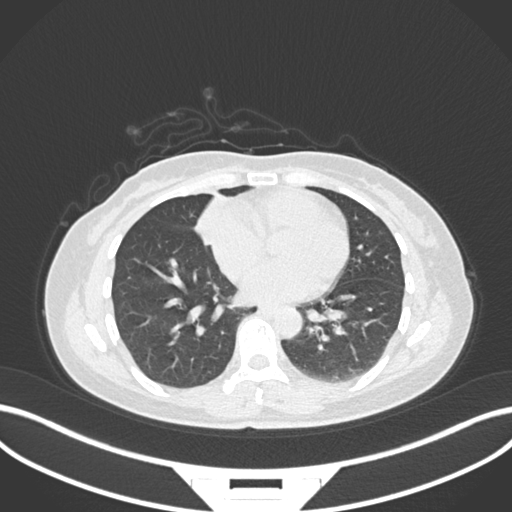
Chest CT, one axial slice. Position 61 of 171 along the scan axis. Reconstruction kernel B30f. Lung window (W 1500 / L -600 HU). 1 mm slice thickness. 512 × 512 image matrix. Patient: female, 43 years. Case-level facts recorded for this patient, not image findings: clinical TNM (as recorded): T1c N3 M1; histopathological grade: G1.
Outlined on this slice (bounding box drawn by a radiologist):
- lung tumour (recorded histology: adenocarcinoma): bounding box (x1, y1, x2, y2) in pixels: (191, 194, 220, 250)